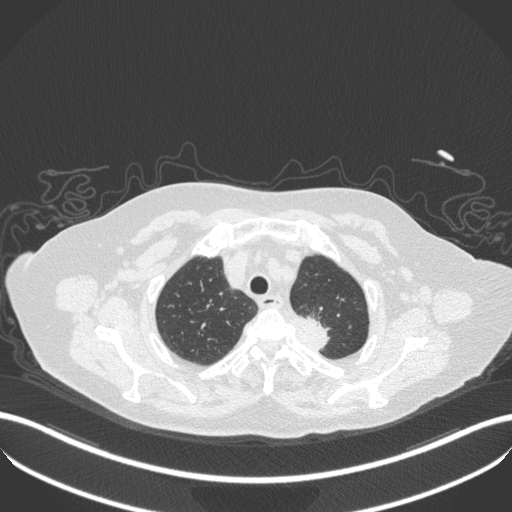
Chest CT, one axial slice; position 289 of 353 along the scan axis; 100 kVp; lung window (W 1500 / L -600 HU); 1 mm slice thickness; 512 × 512 image matrix, field of view 400 × 400 mm. Patient: female, 81 years. Case-level facts recorded for this patient, not image findings: clinical TNM (as recorded): T2a N0 M0.
Structures marked on this image (rectangle marked by the reading radiologist):
- lung tumour (recorded histology: adenocarcinoma): bounding box <273,301,339,356> (left, top, right, bottom; pixels)